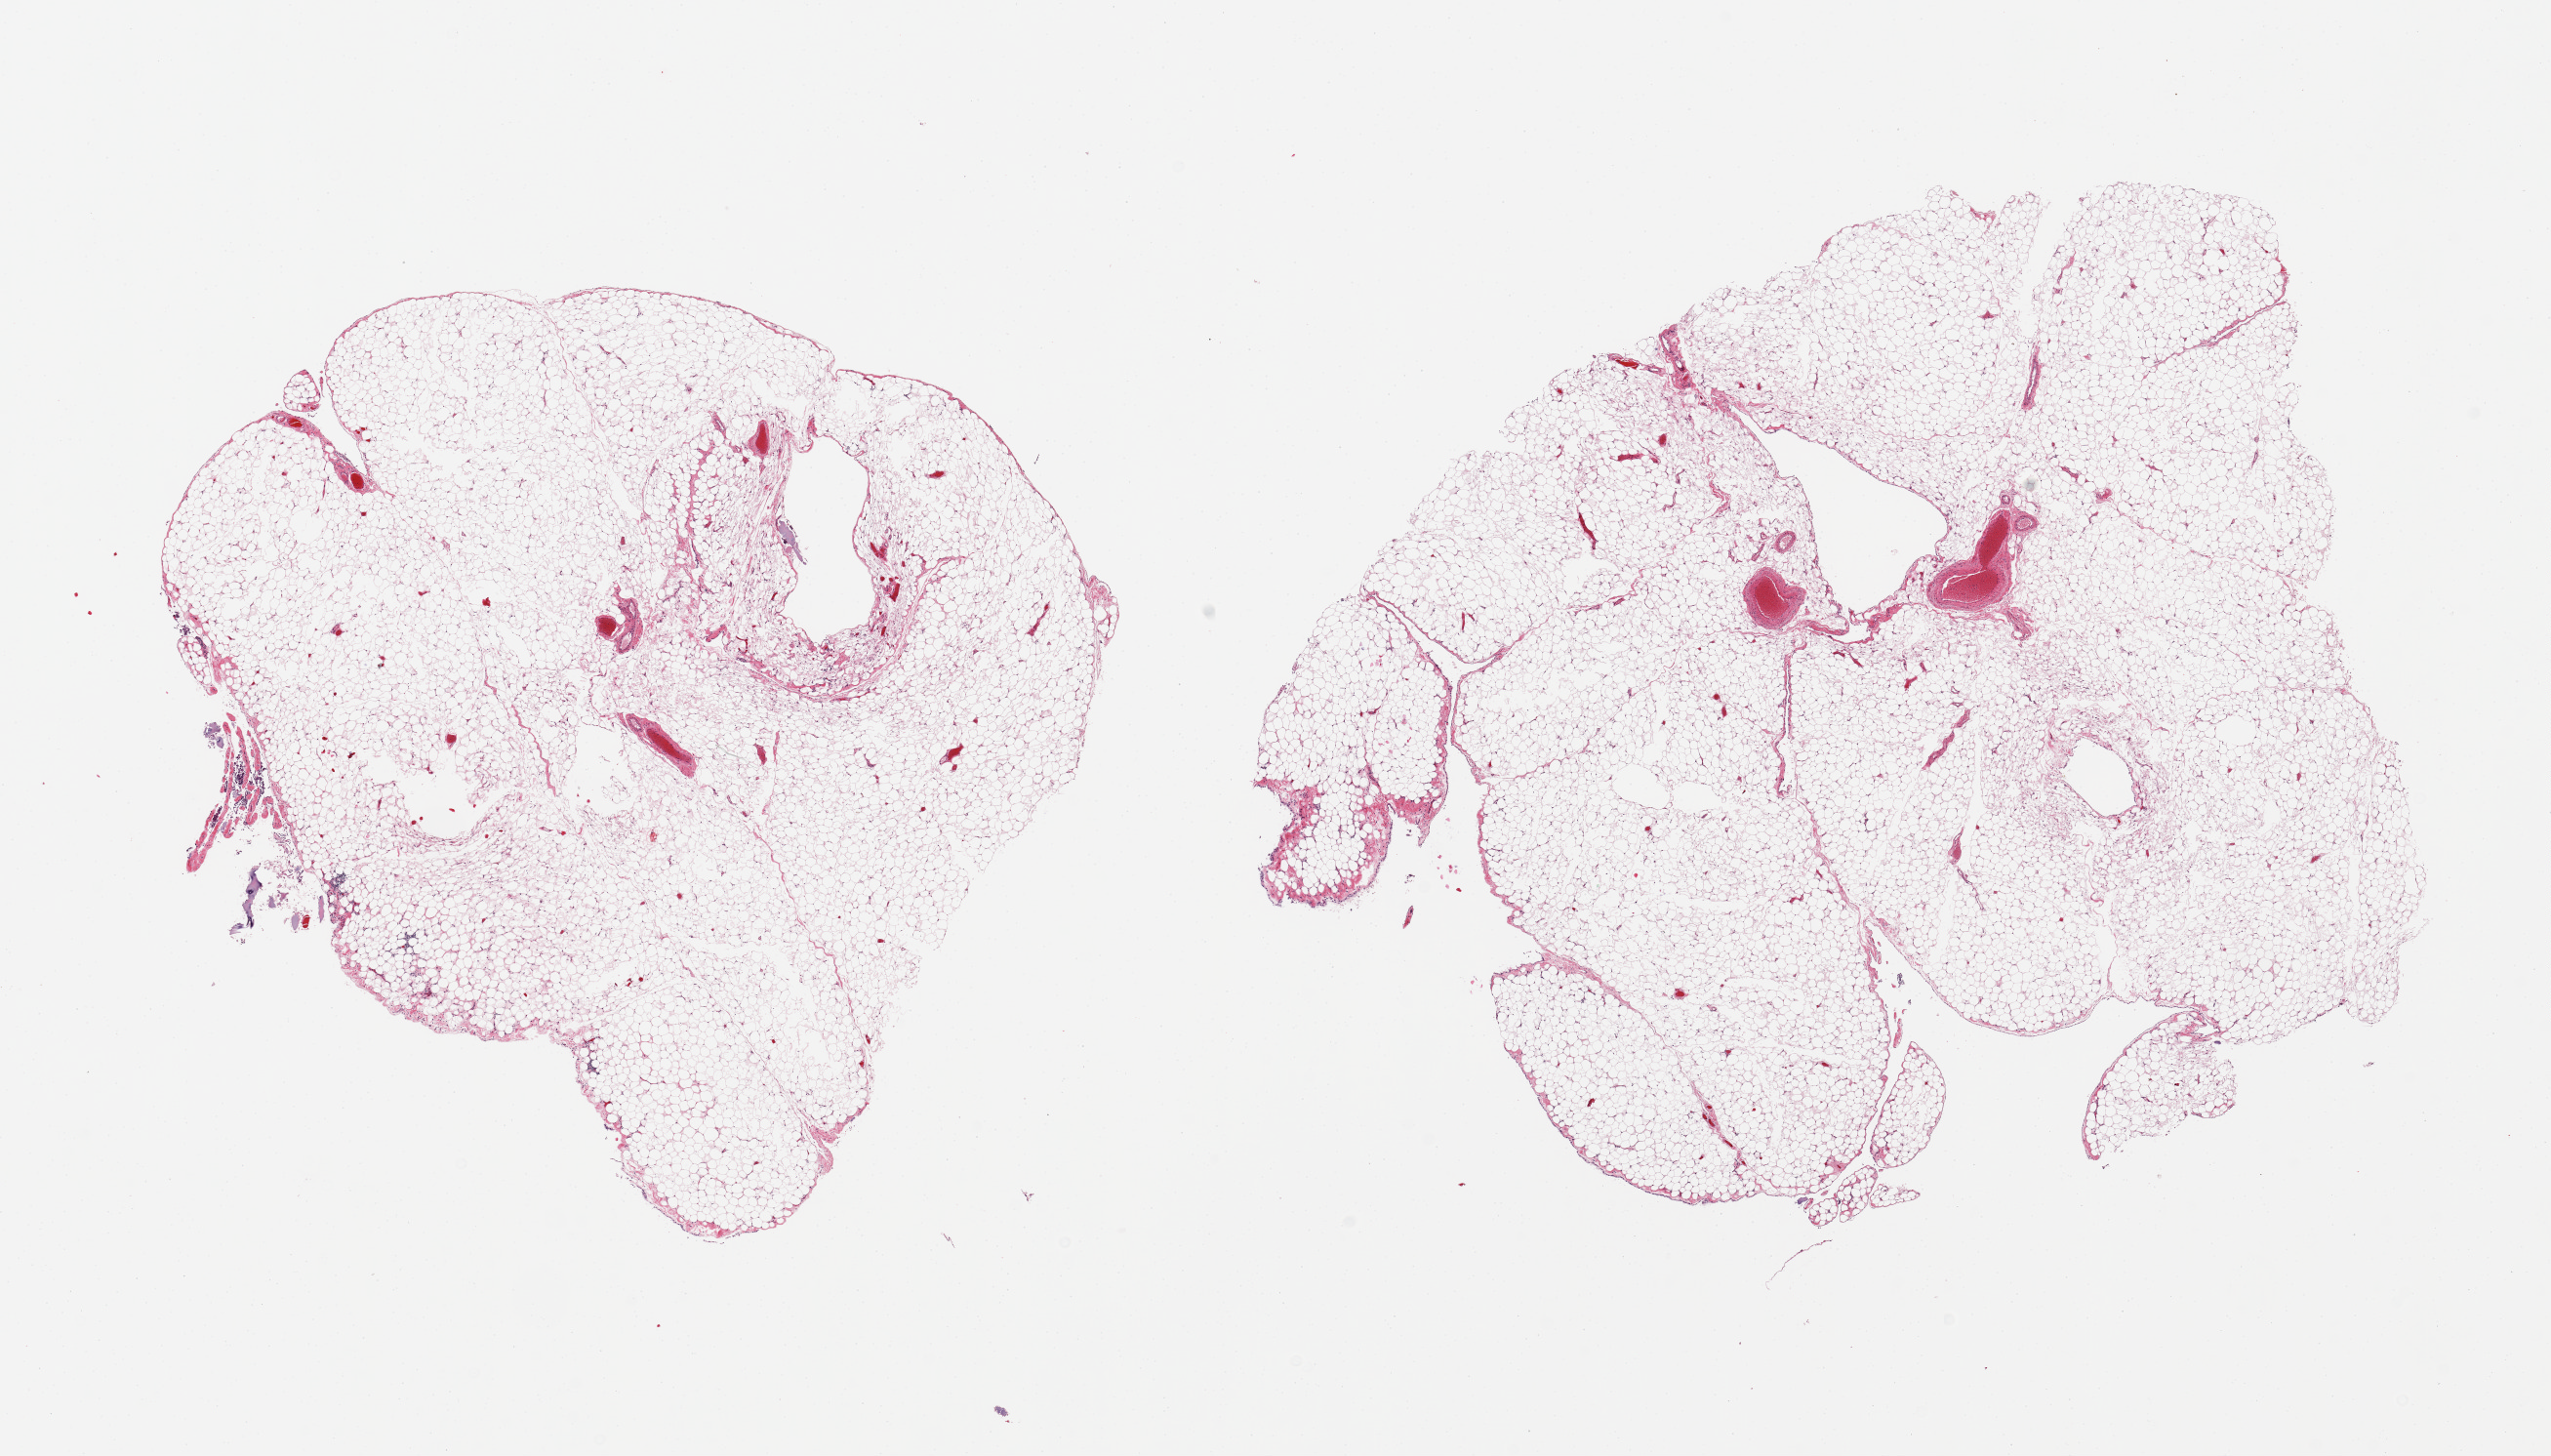
Digitized H&E-stained section — low-resolution overview of the scanned area, about 20.7 x 11.8 mm. PAXgene-fixed paraffin-embedded (PFPE) section. Sampled site (target tissue): omentum. Tissue donor sample.
Reviewer comment on this tissue sample: 2 pieces.